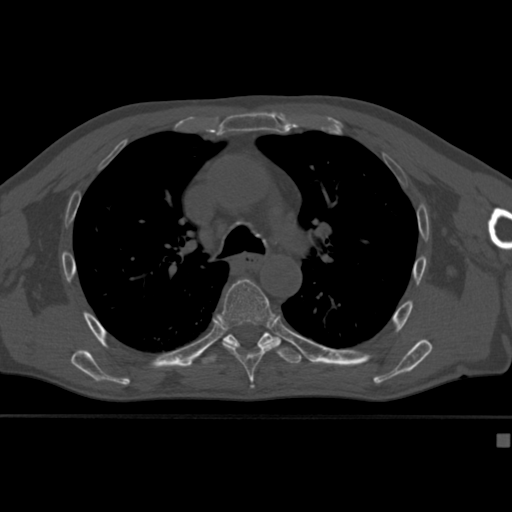
CT including the spine, one axial slice; position 290 of 430 along the scan axis; reconstruction kernel Br40s; bone window (W 1800 / L 400 HU); 1.5 mm slice thickness; 512 × 512 image matrix. Male patient, age 64 years. From the clinical record (not read from this slice): primary cancer: uterus; vertebrae with lytic lesions (as recorded): T1, T4, T5, T7, L5.
Outlined on this slice (semi-automatically segmented with operator editing):
- T6 vertebra: bounding box [x1, y1, x2, y2] px = [214, 279, 281, 382]
- T7 vertebra: [201, 332, 302, 367]